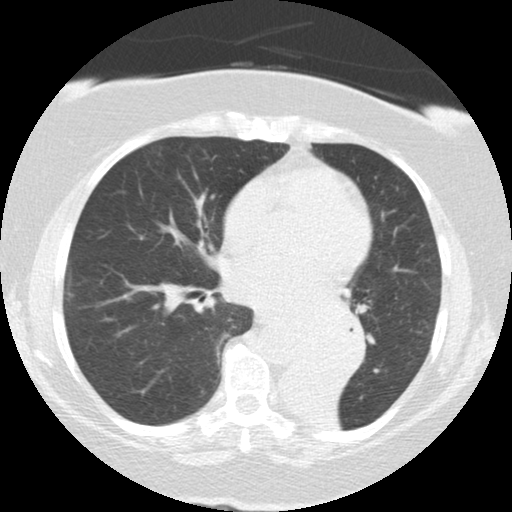
Chest CT (low-dose screening protocol), one axial image; baseline screening round; lung window (W 1500 / L -600 HU); standard (soft-tissue) reconstruction kernel (STANDARD). Female, age 71 years at enrolment. Former smoker at enrolment.
Lesion marked by an expert reader, box from (x=283, y=305) to (x=366, y=383) px. Reader record for this screening exam (exam-level; its link to the box is not recorded): non-calcified nodule or mass ≥4 mm, right middle lobe, 5 × 5 mm, smooth margins, soft tissue attenuation. Note: the box lies in the patient's left hemithorax on this image, whereas the reader's record names the right lung; they may be different findings. Official screen result: positive, change unspecified: nodule(s) >= 4 mm or enlarging nodule(s), mass(es), or other non-specific abnormalities suspicious for lung cancer. Later outcome: lung cancer diagnosed 46 days after this screen — large cell carcinoma, NOS, left lower lobe, mediastinum, other location, poorly differentiated (G3), stage IV (AJCC 6th edition), 50 mm at pathology.